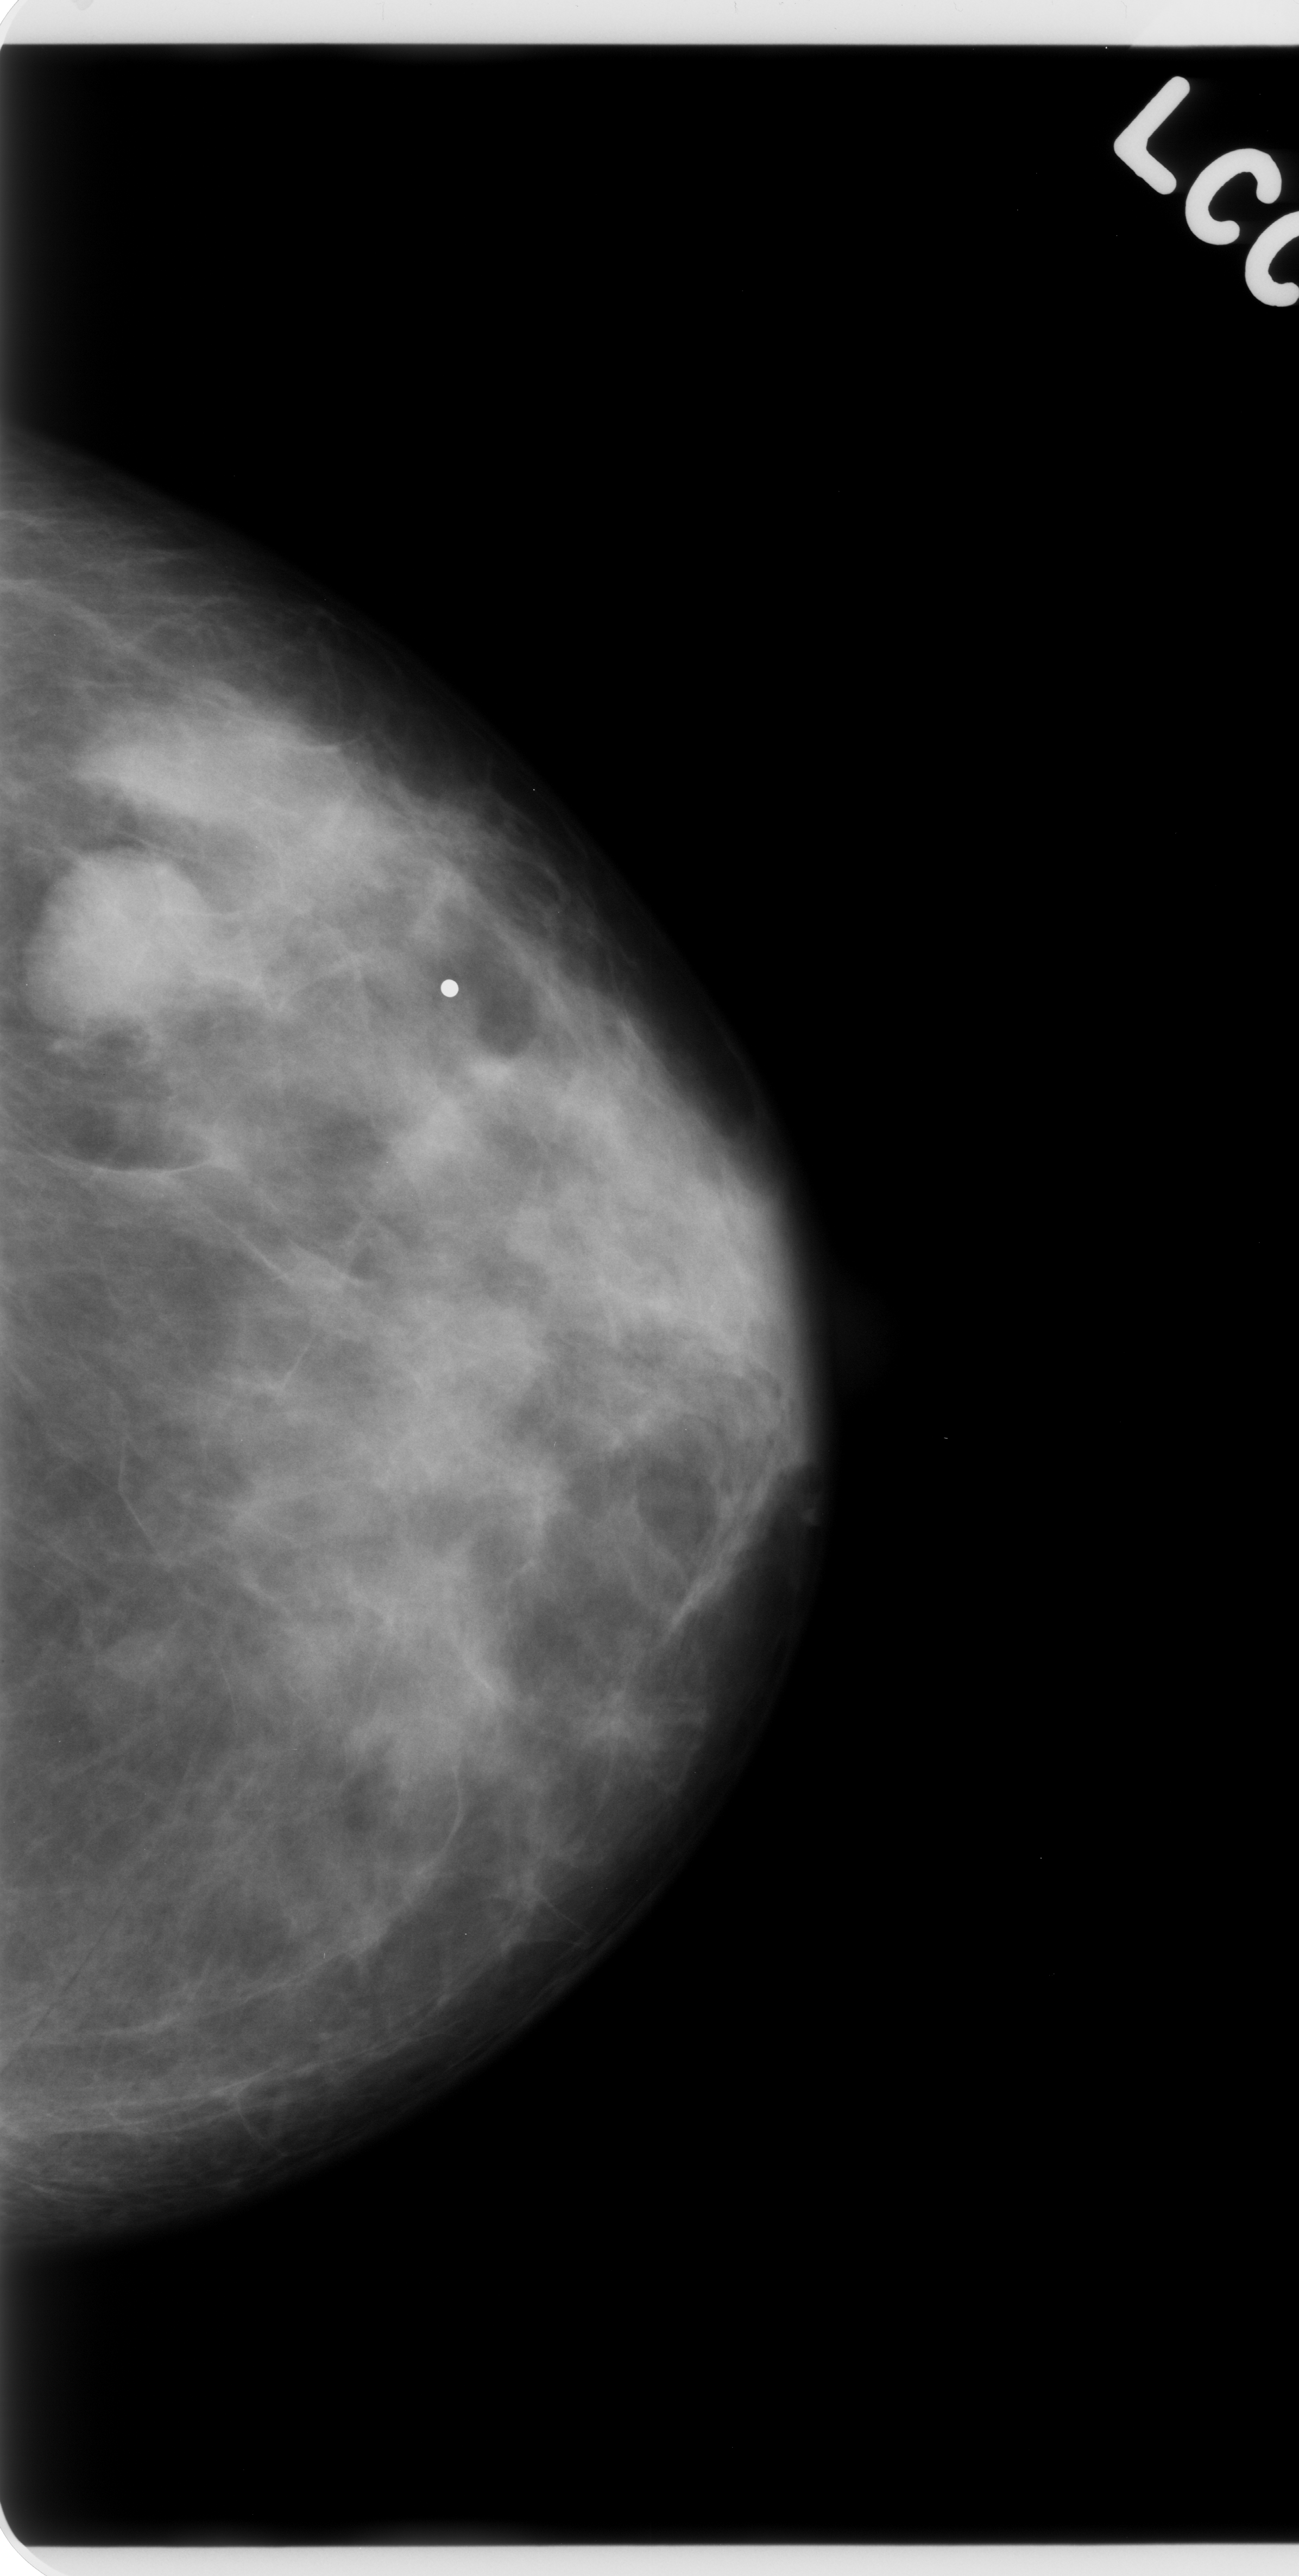
Mammogram (digitized film); left breast; craniocaudal (CC) view; BI-RADS breast density category 2 (scale 1–4); 1299 × 2576 image matrix.
Expert-marked regions of interest on this image (one box per marked abnormality):
- mass, shape oval, margins circumscribed; BI-RADS assessment category 4; subtlety rating 5 on a 1 (subtle) to 5 (obvious) scale; pathology (as recorded): malignant: bounding box [x1, y1, x2, y2] px = [39, 848, 227, 1044]